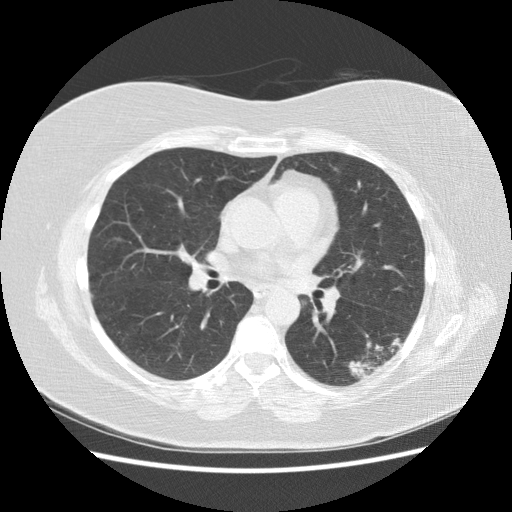
Low-dose screening chest CT, one axial slice. Slice 82 of 151 in the series (ordered by position). 120 kVp. Lung window (W 1500 / L -600 HU). 2.5 mm slice thickness. 512 × 512 image matrix, field of view 360 × 360 mm.
Outlined on this slice (expert manual segmentation):
- lesion 1 (tumor, lower lobe of left lung): box from (x=349, y=337) to (x=406, y=378) px